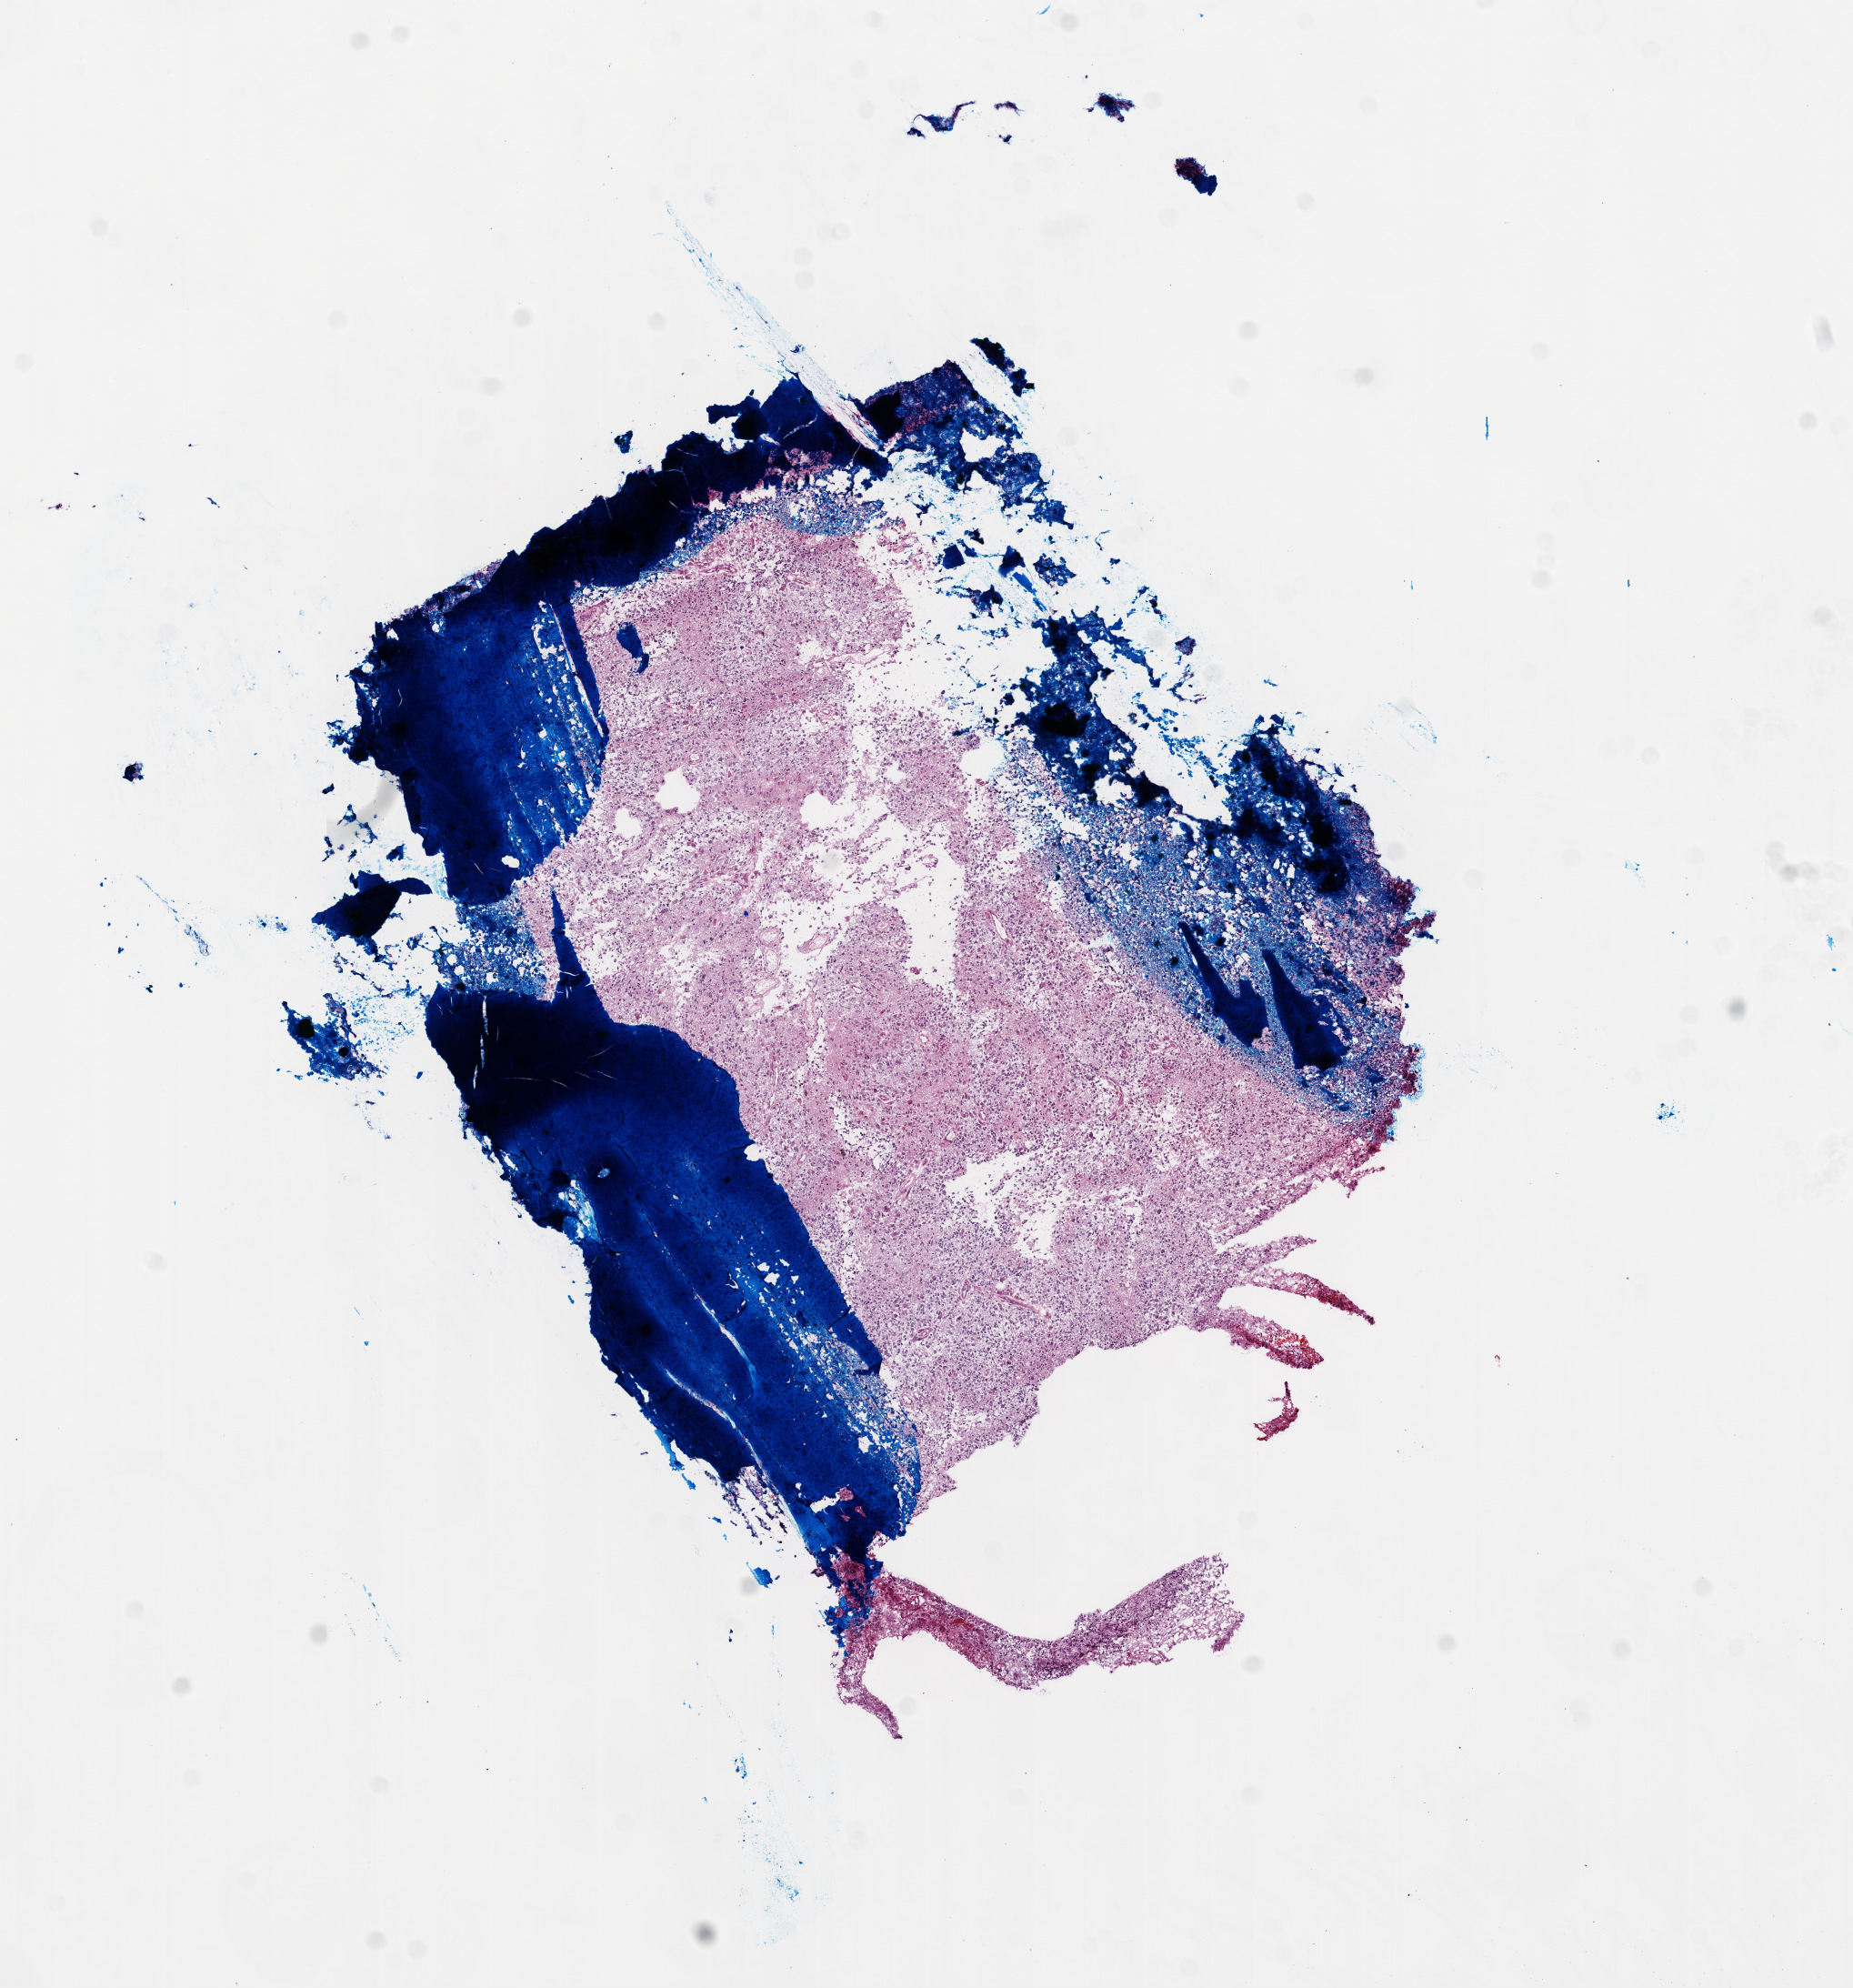
Hematoxylin and eosin (H&E) stained whole-slide image — low-resolution overview of the scanned area, about 8.2 x 8.8 mm. Frozen section. Primary tumour sample from the brain. Male patient; age at initial diagnosis 77 years. Slide review estimates, as recorded: tumour cells 90%, tumour nuclei 100%, normal cells 0%, stromal cells 0%, necrosis 10%.
Diagnosis: Glioblastoma.